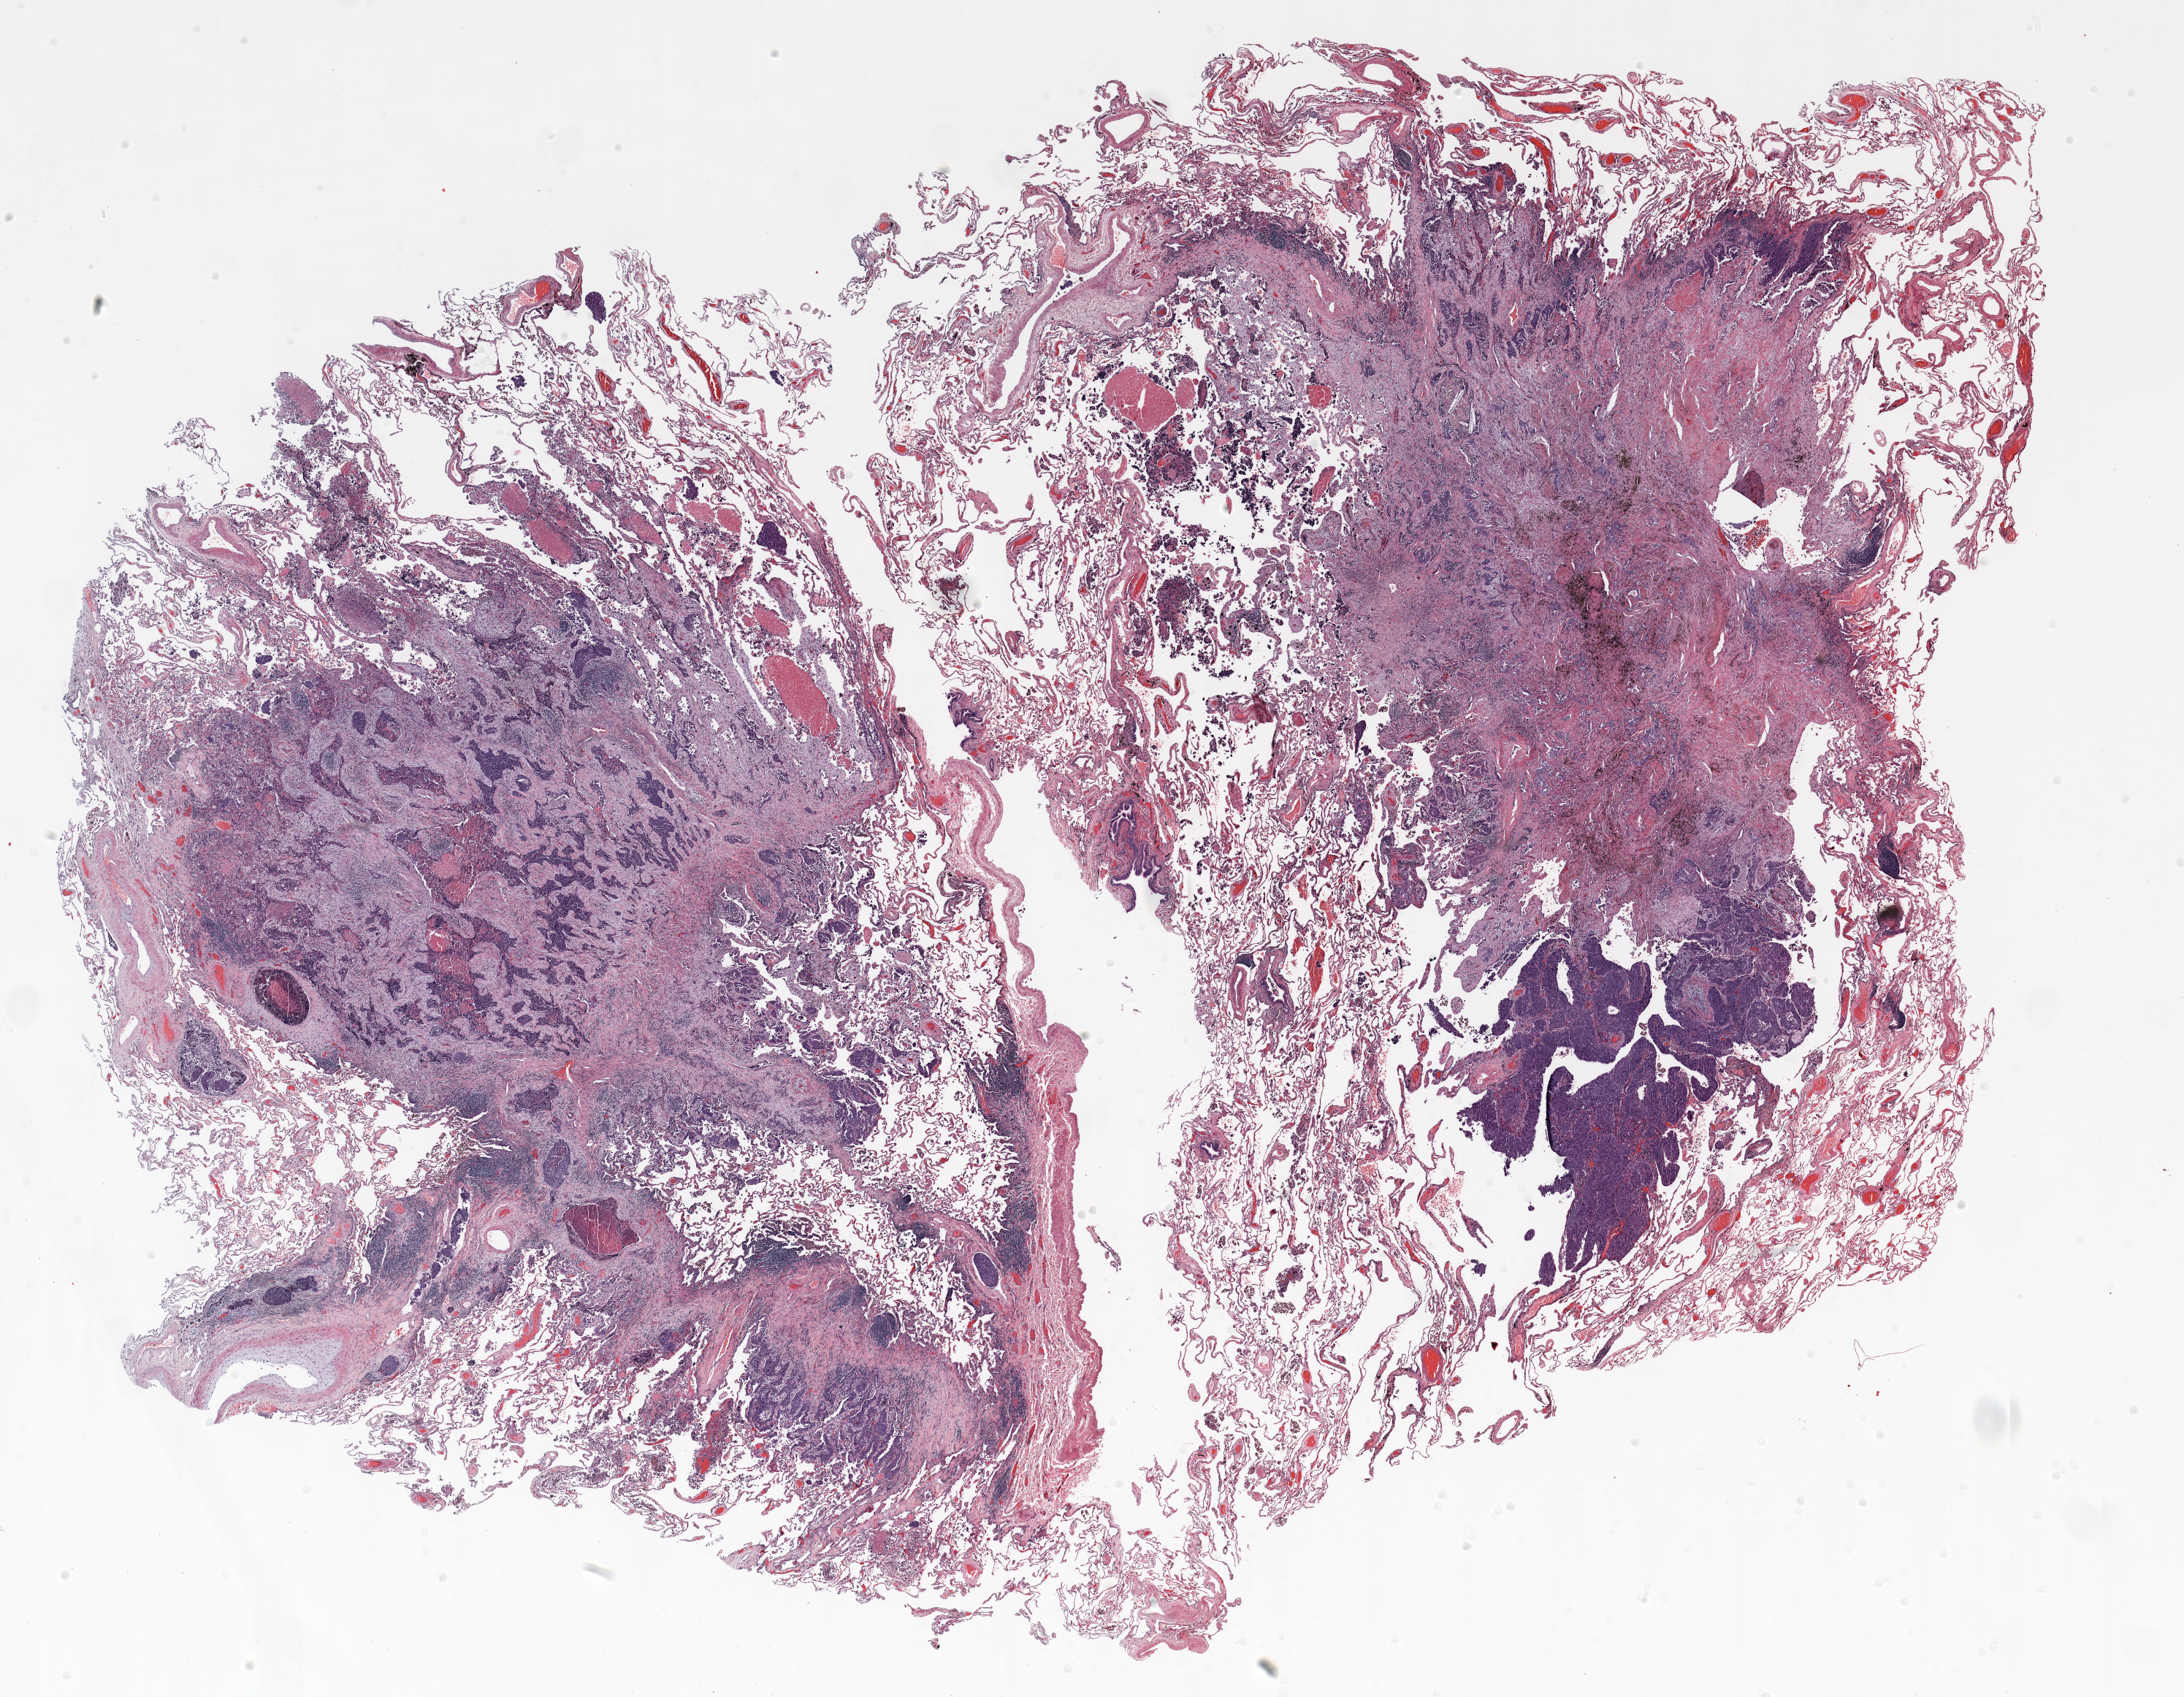
Whole-slide histology image, H&E, a low-resolution overview of the entire scanned area, about 24.0 x 18.7 mm (acquisition: 20x scan); formalin-fixed paraffin-embedded (FFPE) section; lung tissue. Male patient, aged 66 at enrolment.
Participant's lung-cancer diagnosis: Squamous cell carcinoma, NOS.